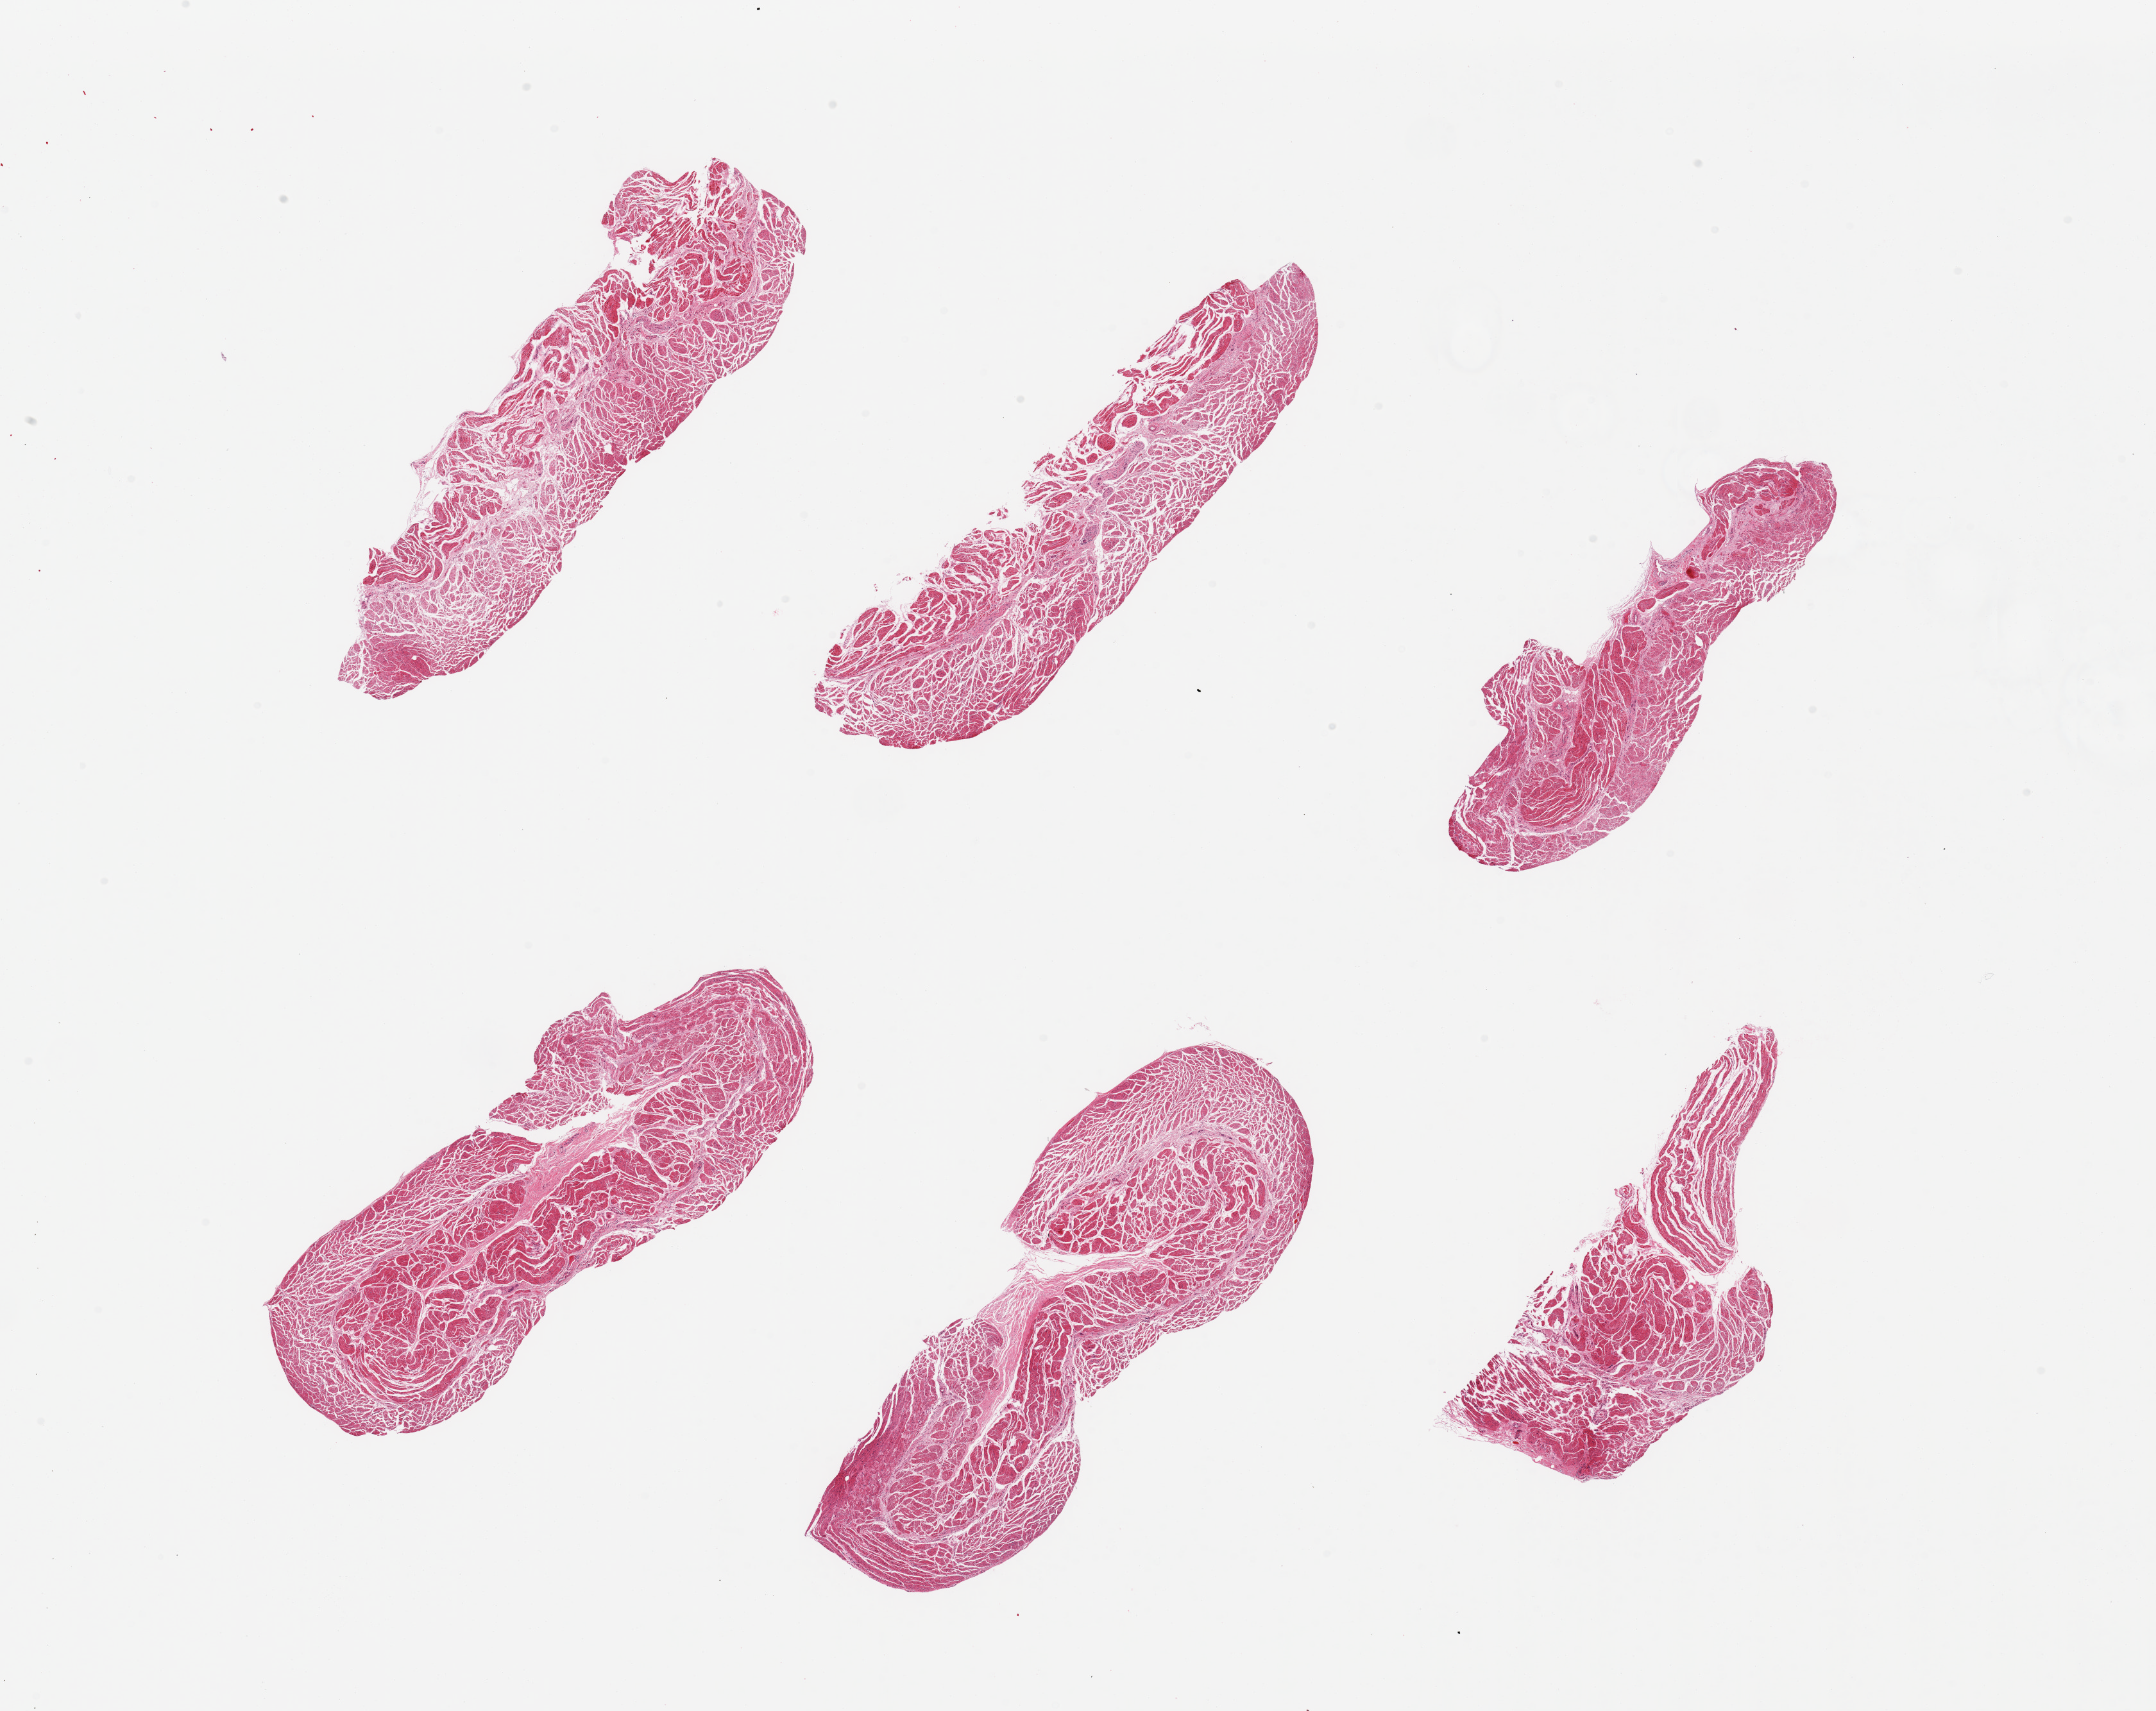
Whole-slide image, haematoxylin and eosin stain, brightfield — low-resolution overview of the scanned area, about 26.6 x 21.1 mm (from a 20x scan); PAXgene-fixed paraffin-embedded (PFPE) section; sampled site (target tissue): esophageal muscle; donor tissue sample. Donor: male.
Reviewer comment on this tissue sample: 6 pieces; mild to moderate autolysis; well trimmed target muscularis.